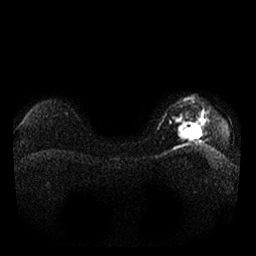
Breast MRI, one axial slice. Slice 20 of 25 in the series (ordered by position). Diffusion-weighted series; image 2 of 4 stored at this slice position (different b-values; order by instance number). 1.5 T. 4 mm slice thickness. 256 × 256 image matrix, field of view 340 × 340 mm. Female patient.
Outlined on this slice (manually delineated by an expert):
- tumour on diffusion-weighted imaging: bounding box (x1, y1, x2, y2) in pixels: (176, 120, 202, 142)